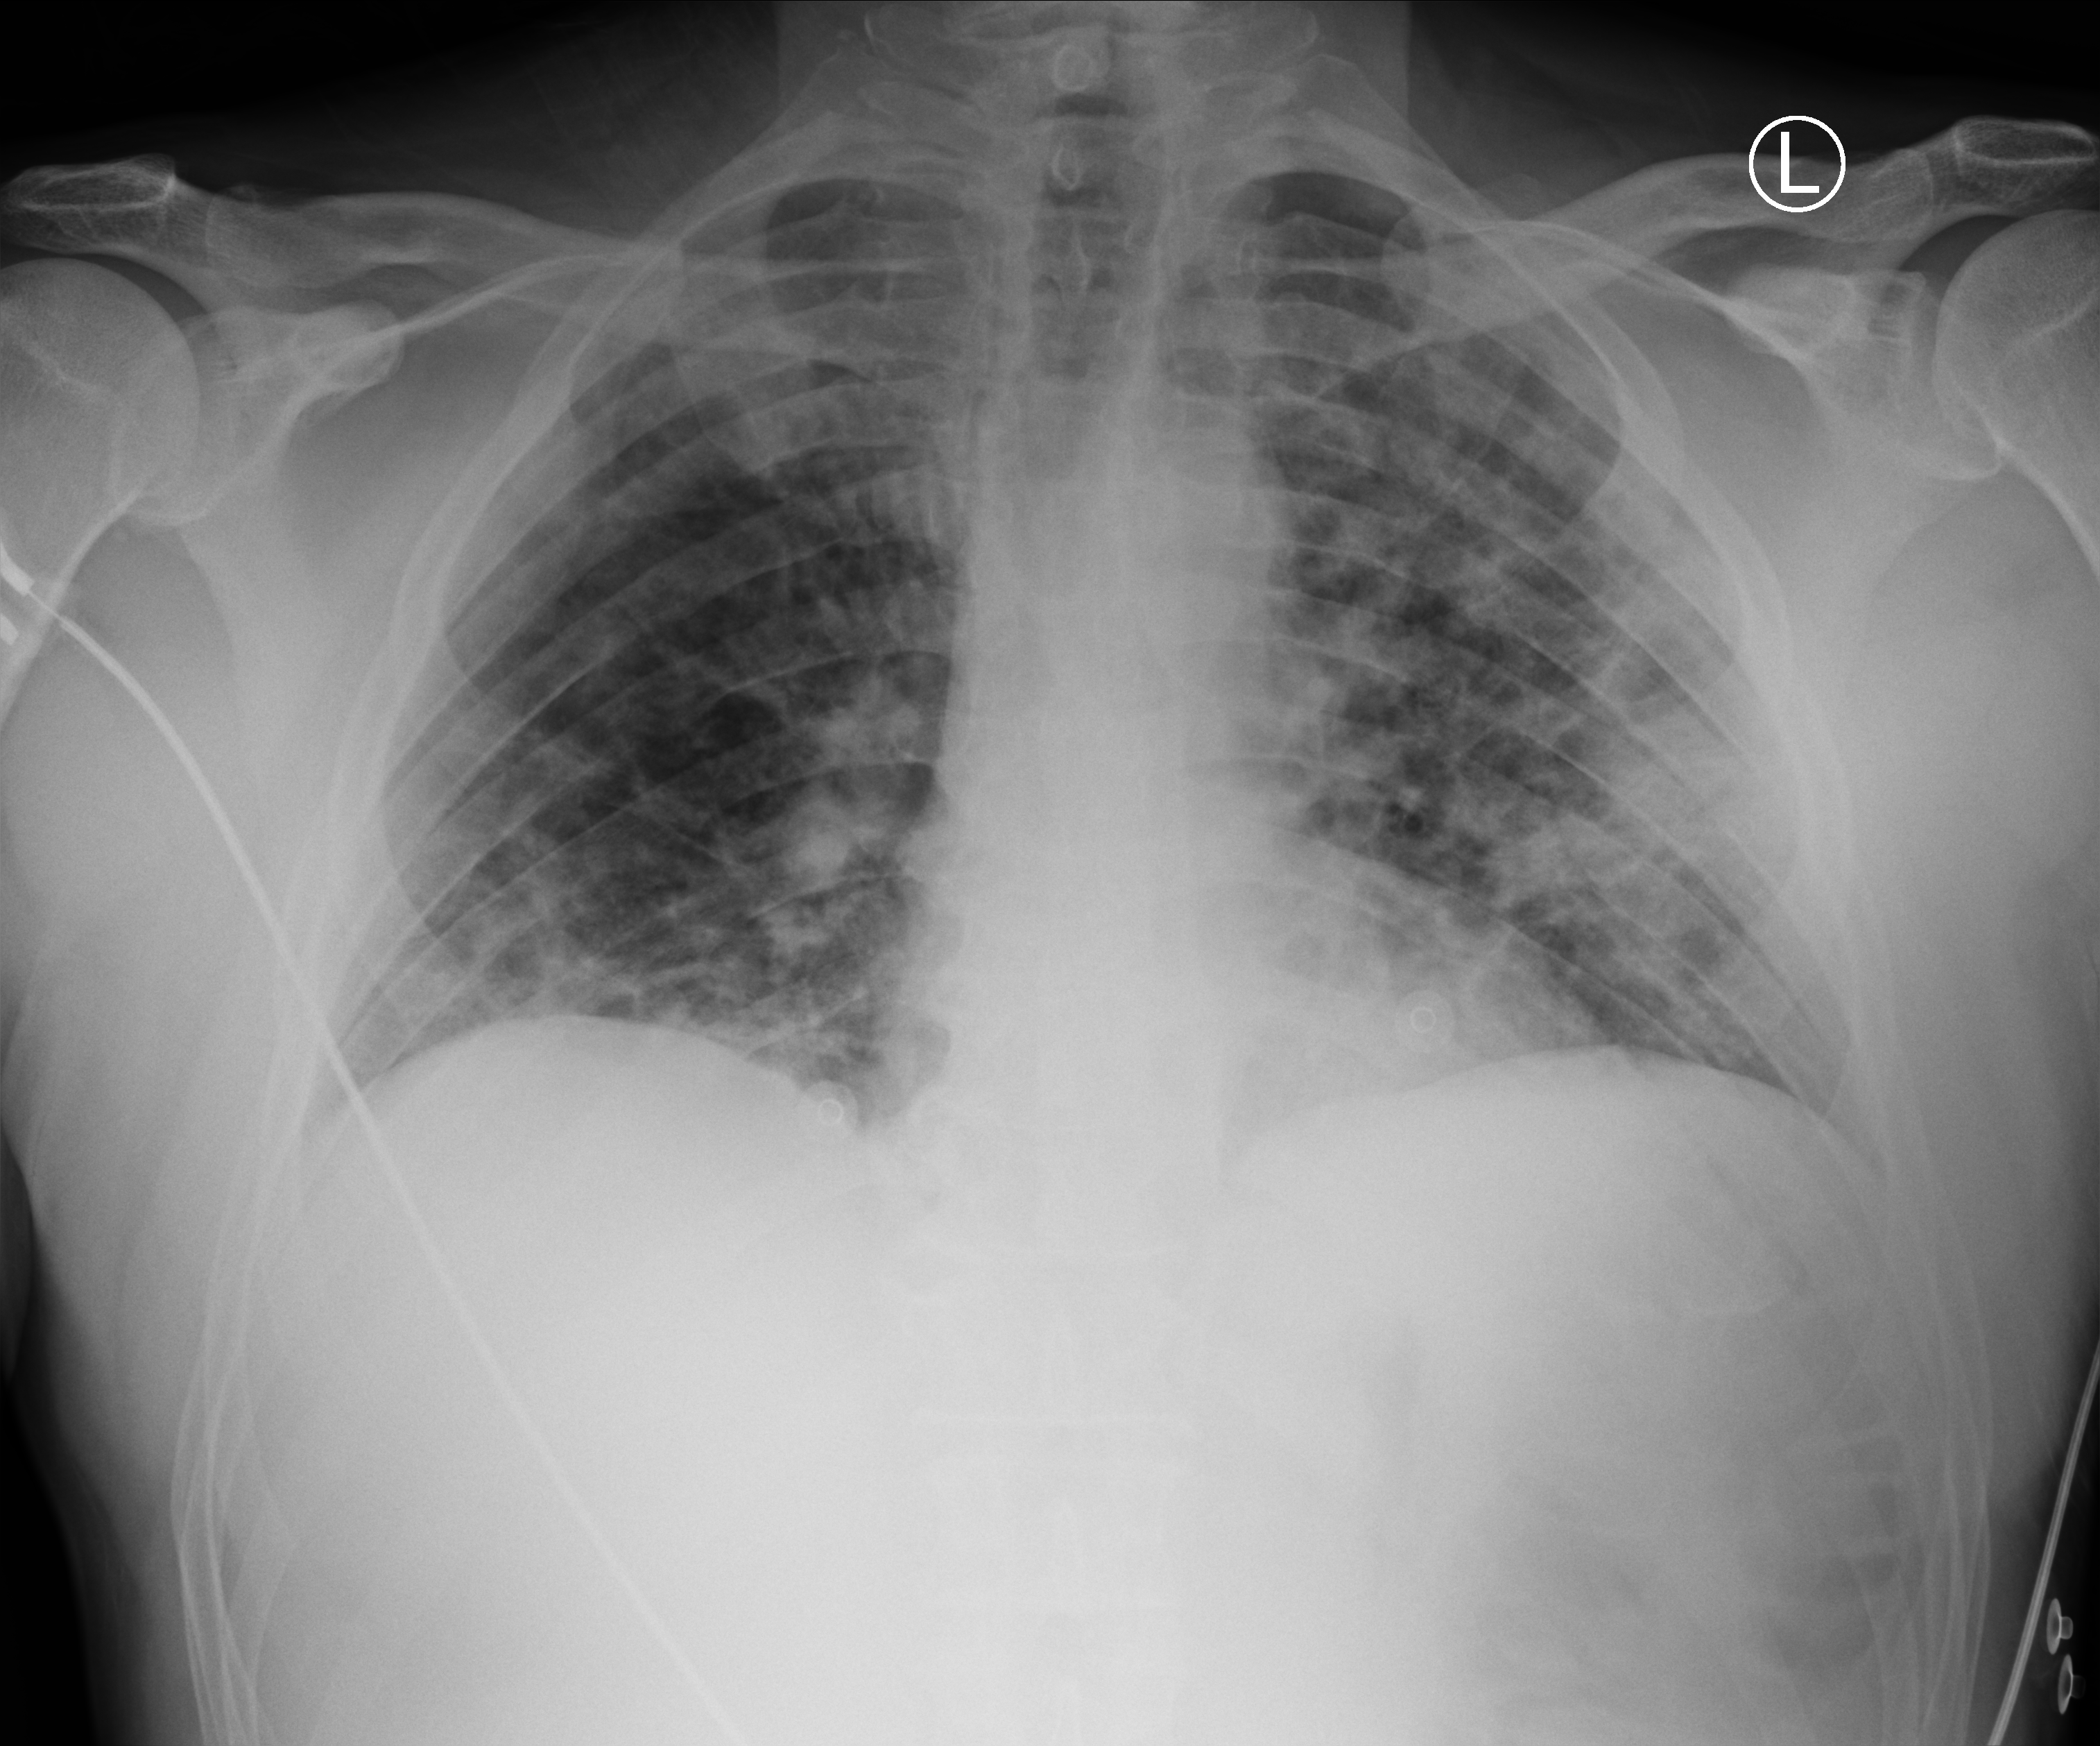
Portable chest radiograph. Patient hospitalised with COVID-19; male, aged 18–59 years.
Hospital-stay facts (about this admission, not read from this image; timing relative to this image not recorded): admitted to intensive care during this hospital stay: no; mechanically ventilated during this hospital stay: no; COPD (admission record): no.